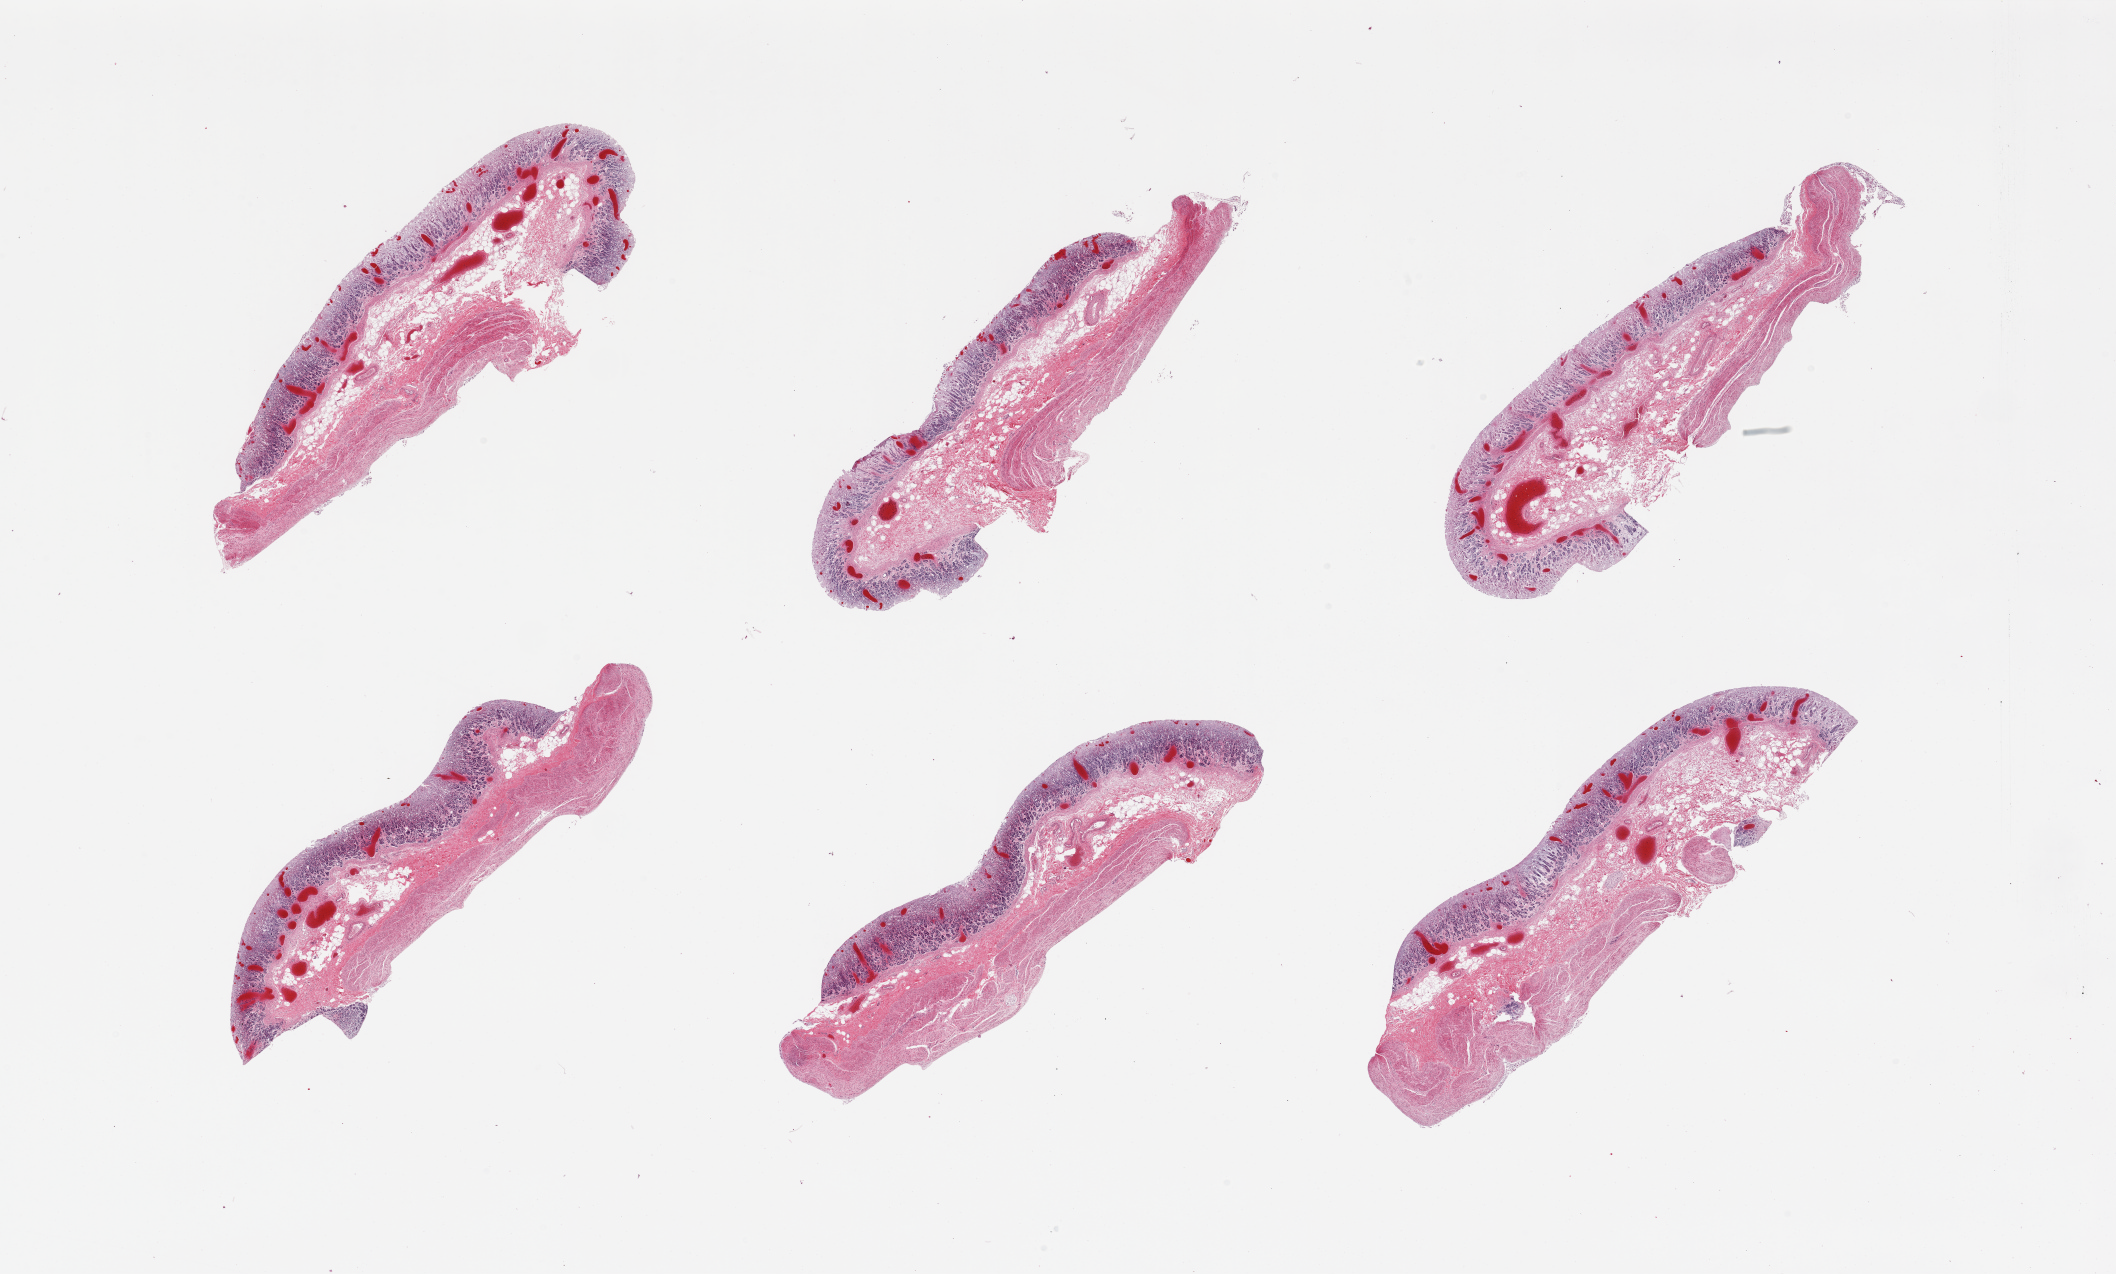
Hematoxylin and eosin (H&E) whole-slide image, brightfield, a low-resolution overview of the entire scanned area, about 33.5 x 20.2 mm, PAXgene-fixed, paraffin-embedded tissue, sampled site (target tissue): stomach, tissue donor sample. Female donor.
Reviewer comment on this tissue sample: 6 pieces, markedly autolyzed, congested.